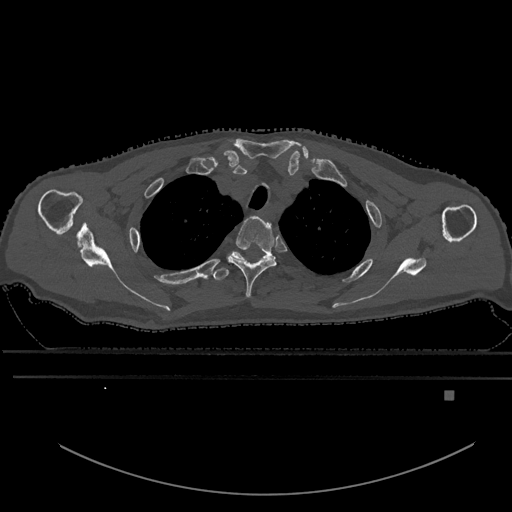
CT including the spine, one axial slice. Slice 487 of 969 in the series (ordered by position). Bone window (W 1800 / L 400 HU). 0.5 mm slice thickness. 512 × 512 image matrix, field of view 456 × 456 mm. Male patient, age 82 years. Case-level facts recorded for this patient, not image findings: primary cancer: prostate; vertebrae with lytic lesions (as recorded): T11, T9, T8, T2.
Annotated regions visible in this slice (semi-automatically segmented with operator editing):
- T2 vertebra: bounding box (x1, y1, x2, y2) in pixels: (227, 215, 277, 299)
- T3 vertebra: (212, 252, 264, 281)